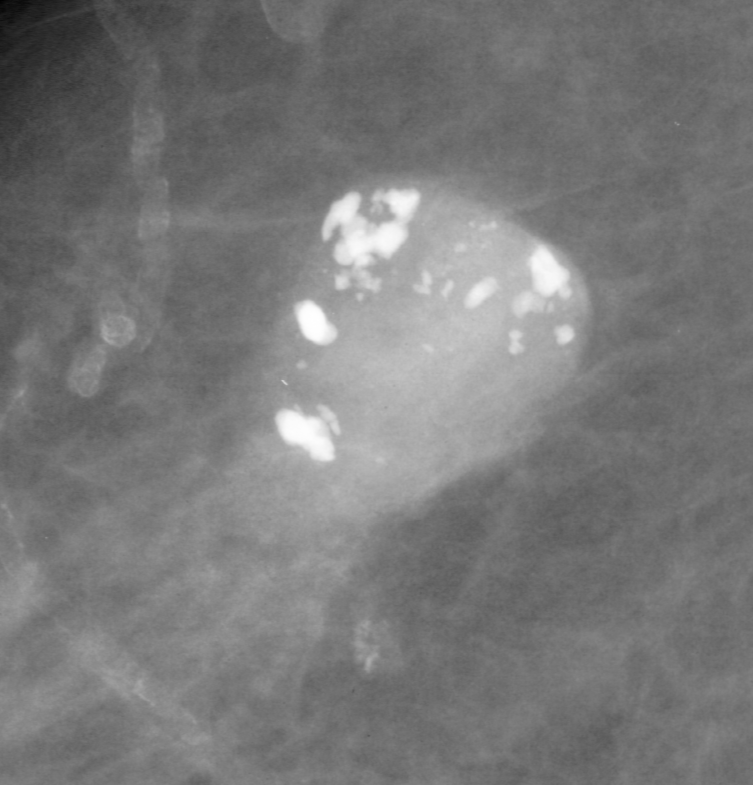
Crop from a digitized film mammogram around one marked abnormality, left breast, CC view.
- Finding: calcifications, morphology amorphous; BI-RADS assessment category 2; subtlety rating 5 on a 1 (subtle) to 5 (obvious) scale; pathology result (as recorded, not read from the image): benign.